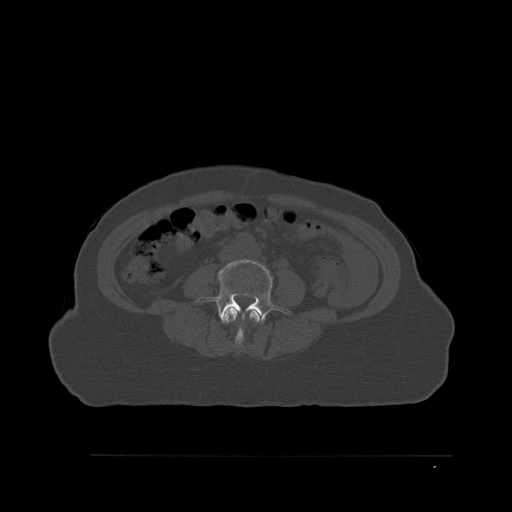
CT including the spine, one axial slice. Slice 212 of 527 in the series (ordered by position). Bone window (W 1800 / L 400 HU). 1.5 mm slice thickness. 512 × 512 image matrix, field of view 470 × 470 mm. Female patient, age 73 years. Case-level facts recorded for this patient, not image findings: primary cancer: breast.
Outlined on this slice (semi-automatic segmentation, software-assisted and operator-edited):
- L3 vertebra: bounding box [x1, y1, x2, y2] px = [224, 306, 261, 346]
- L4 vertebra: [196, 258, 290, 328]